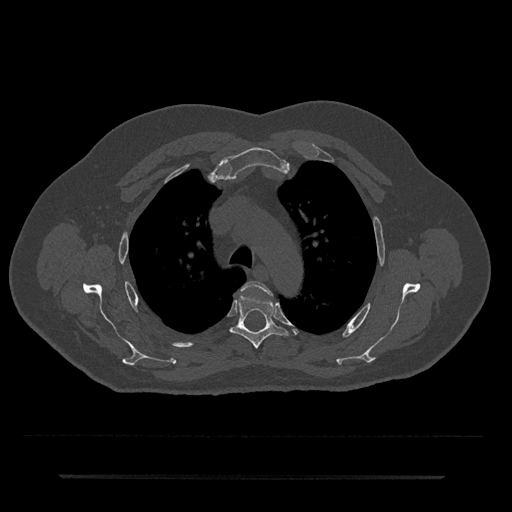
CT including the spine, one axial slice; position 531 of 797 along the scan axis; reconstruction kernel Br40s/3; 120 kVp; bone window (W 1800 / L 400 HU); 0.5 mm slice thickness; 512 × 512 image matrix, field of view 437 × 437 mm. Male patient, age 69 years. Case-level facts recorded for this patient, not image findings: primary cancer: prostate.
Outlined on this slice (semi-automatically segmented with operator editing):
- T3 vertebra: bounding box (x1, y1, x2, y2) in pixels: (242, 281, 272, 295)
- T4 vertebra: (230, 295, 289, 349)